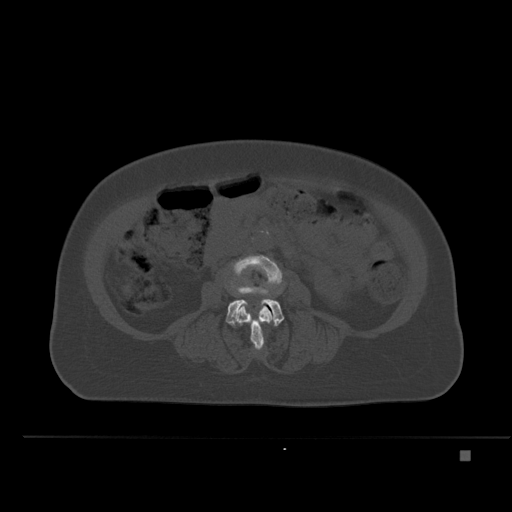
CT including the spine, one axial slice. Slice 188 of 477 in the series (ordered by position). Bone window (W 1800 / L 400 HU). 512 × 512 image matrix, field of view 422 × 422 mm. Female patient, age 74 years. Case-level facts recorded for this patient, not image findings: primary cancer: colon.
Structures marked on this image (semi-automatic segmentation, software-assisted and operator-edited):
- L3 vertebra: bounding box [x1, y1, x2, y2] px = [227, 255, 283, 350]
- L4 vertebra: [225, 281, 284, 326]